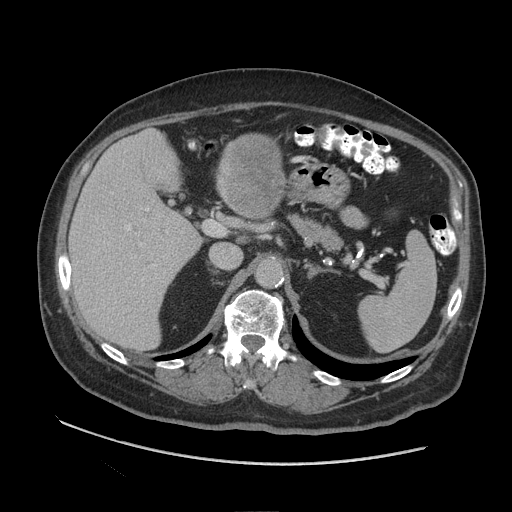
Contrast-enhanced abdominal CT (liver protocol), one axial slice; slice 54 of 109 in the series (ordered by position); reconstruction kernel STANDARD; soft-tissue window (W 400 / L 40 HU); 2.5 mm slice thickness; 512 × 512 image matrix, field of view 420 × 420 mm. Case-level facts recorded for this patient, not image findings: diagnosis: hepatocellular carcinoma (patient treated with transarterial chemoembolisation; whether this scan precedes or follows treatment is not stated here); TNM stage (as recorded): Stage-I; Child-Pugh class: A.
Structures marked on this image (semi-automatic segmentation, software-assisted and operator-edited):
- liver parenchyma outside the tumour (the mass and vessels are separate outlines, so this box may not span the whole liver): bounding box <68,130,200,350> (left, top, right, bottom; pixels)
- mass: <217,132,286,218>
- liver vessels: <125,208,157,280>